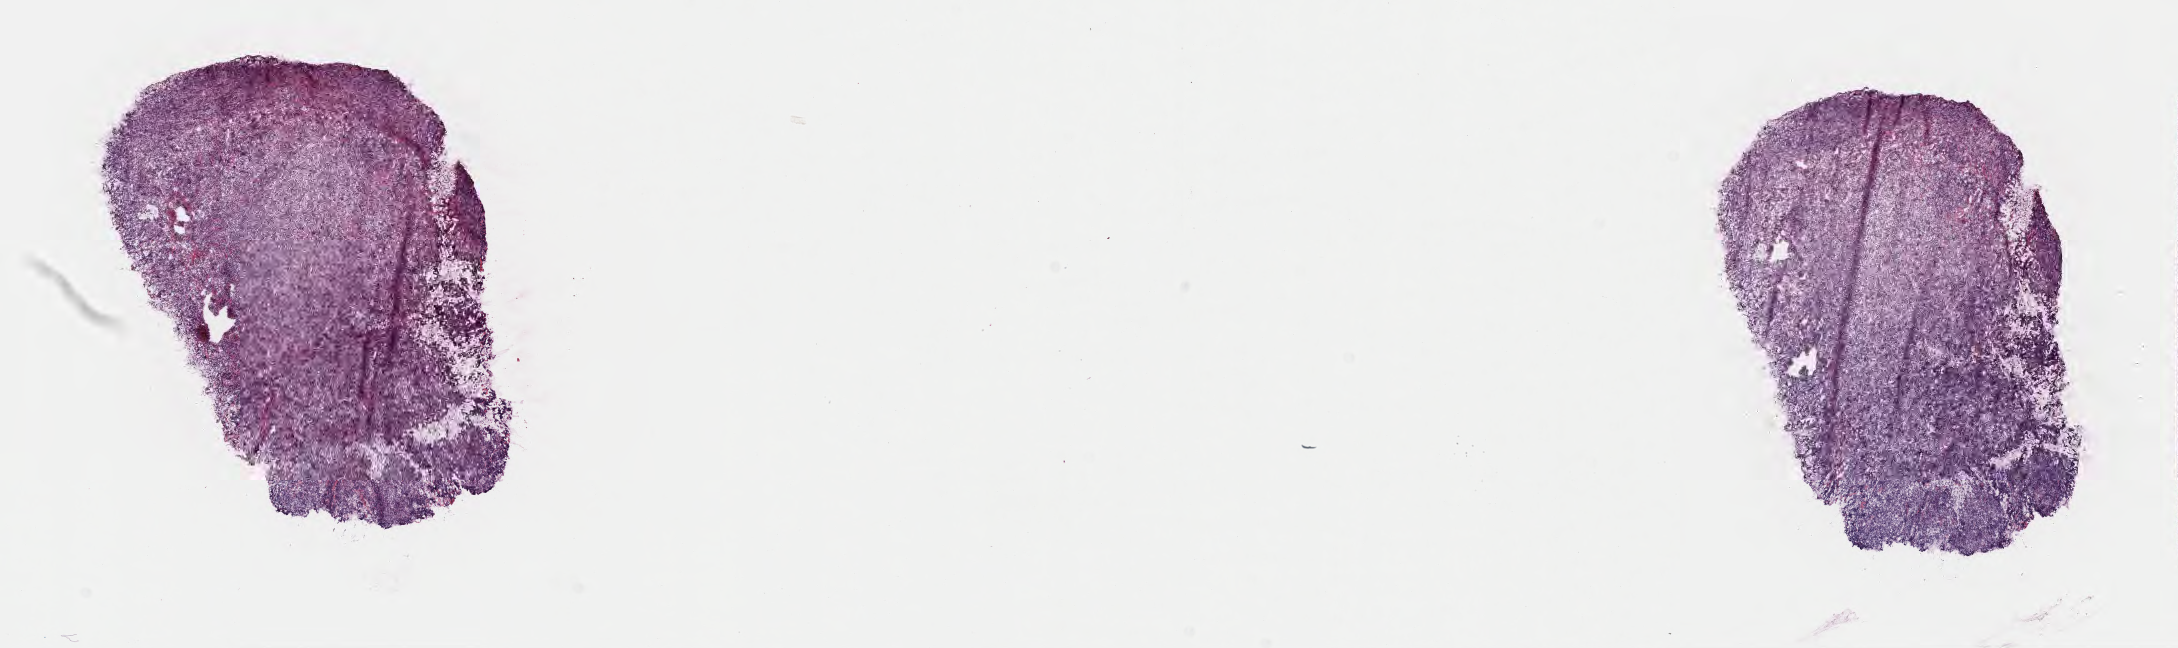
Digitized H&E-stained section — low-resolution overview of the scanned area, about 17.6 x 5.2 mm; cryosection; specimen: primary tumor; site: cranium. Patient female; aged 10. Composition of this section per pathologist review: tumor cells 80%, tumor nuclei 85%, stromal cells 5%, necrosis 15%, normal cells 0%. Infiltration values recorded for this section: lymphocyte infiltration 30%, monocyte infiltration 40%, neutrophil infiltration 5%.
Histologic diagnosis: Diffuse large B-cell lymphoma, NOS. Ann Arbor stage (patient): Stage IV.